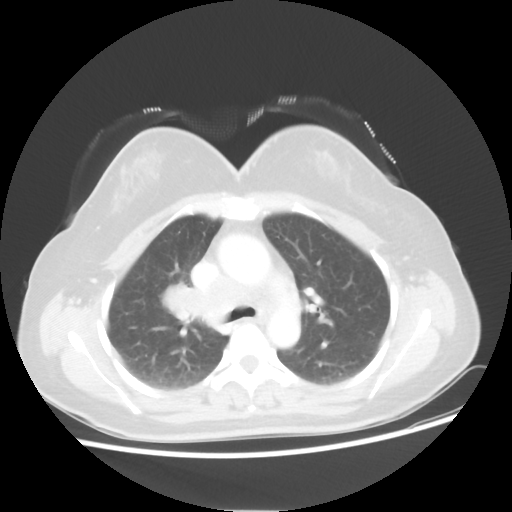
Chest CT, one axial slice. Position 34 of 50 along the scan axis. Reconstruction kernel STANDARD. Lung window (W 1500 / L -600 HU). 512 × 512 image matrix. Female patient, age 40 years. Case-level facts recorded for this patient, not image findings: clinical TNM (as recorded): T1c N3 M0.
Structures marked on this image (rectangle marked by the reading radiologist):
- lung tumour (recorded histology: small cell carcinoma): bounding box (x1, y1, x2, y2) in pixels: (163, 281, 199, 323)